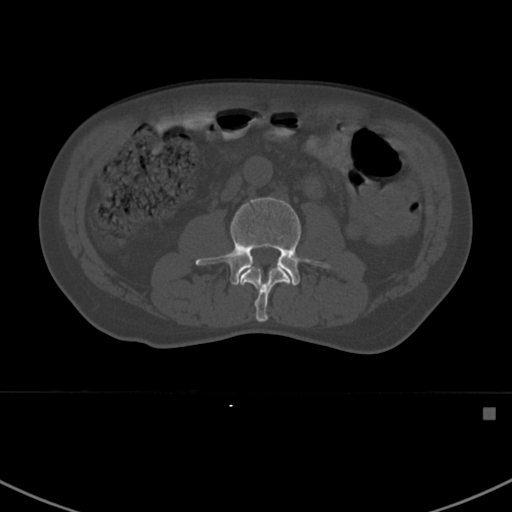
CT including the spine, one axial slice; position 272 of 412 along the scan axis; 120 kVp; bone window (W 1800 / L 400 HU); 1.5 mm slice thickness; 512 × 512 image matrix, field of view 358 × 358 mm. Male patient, age 59 years. From the clinical record (not read from this slice): primary cancer: prostate.
Structures marked on this image (semi-automatic segmentation, software-assisted and operator-edited):
- L2 vertebra: bounding box (x1, y1, x2, y2) in pixels: (240, 266, 290, 322)
- L3 vertebra: (195, 197, 331, 286)